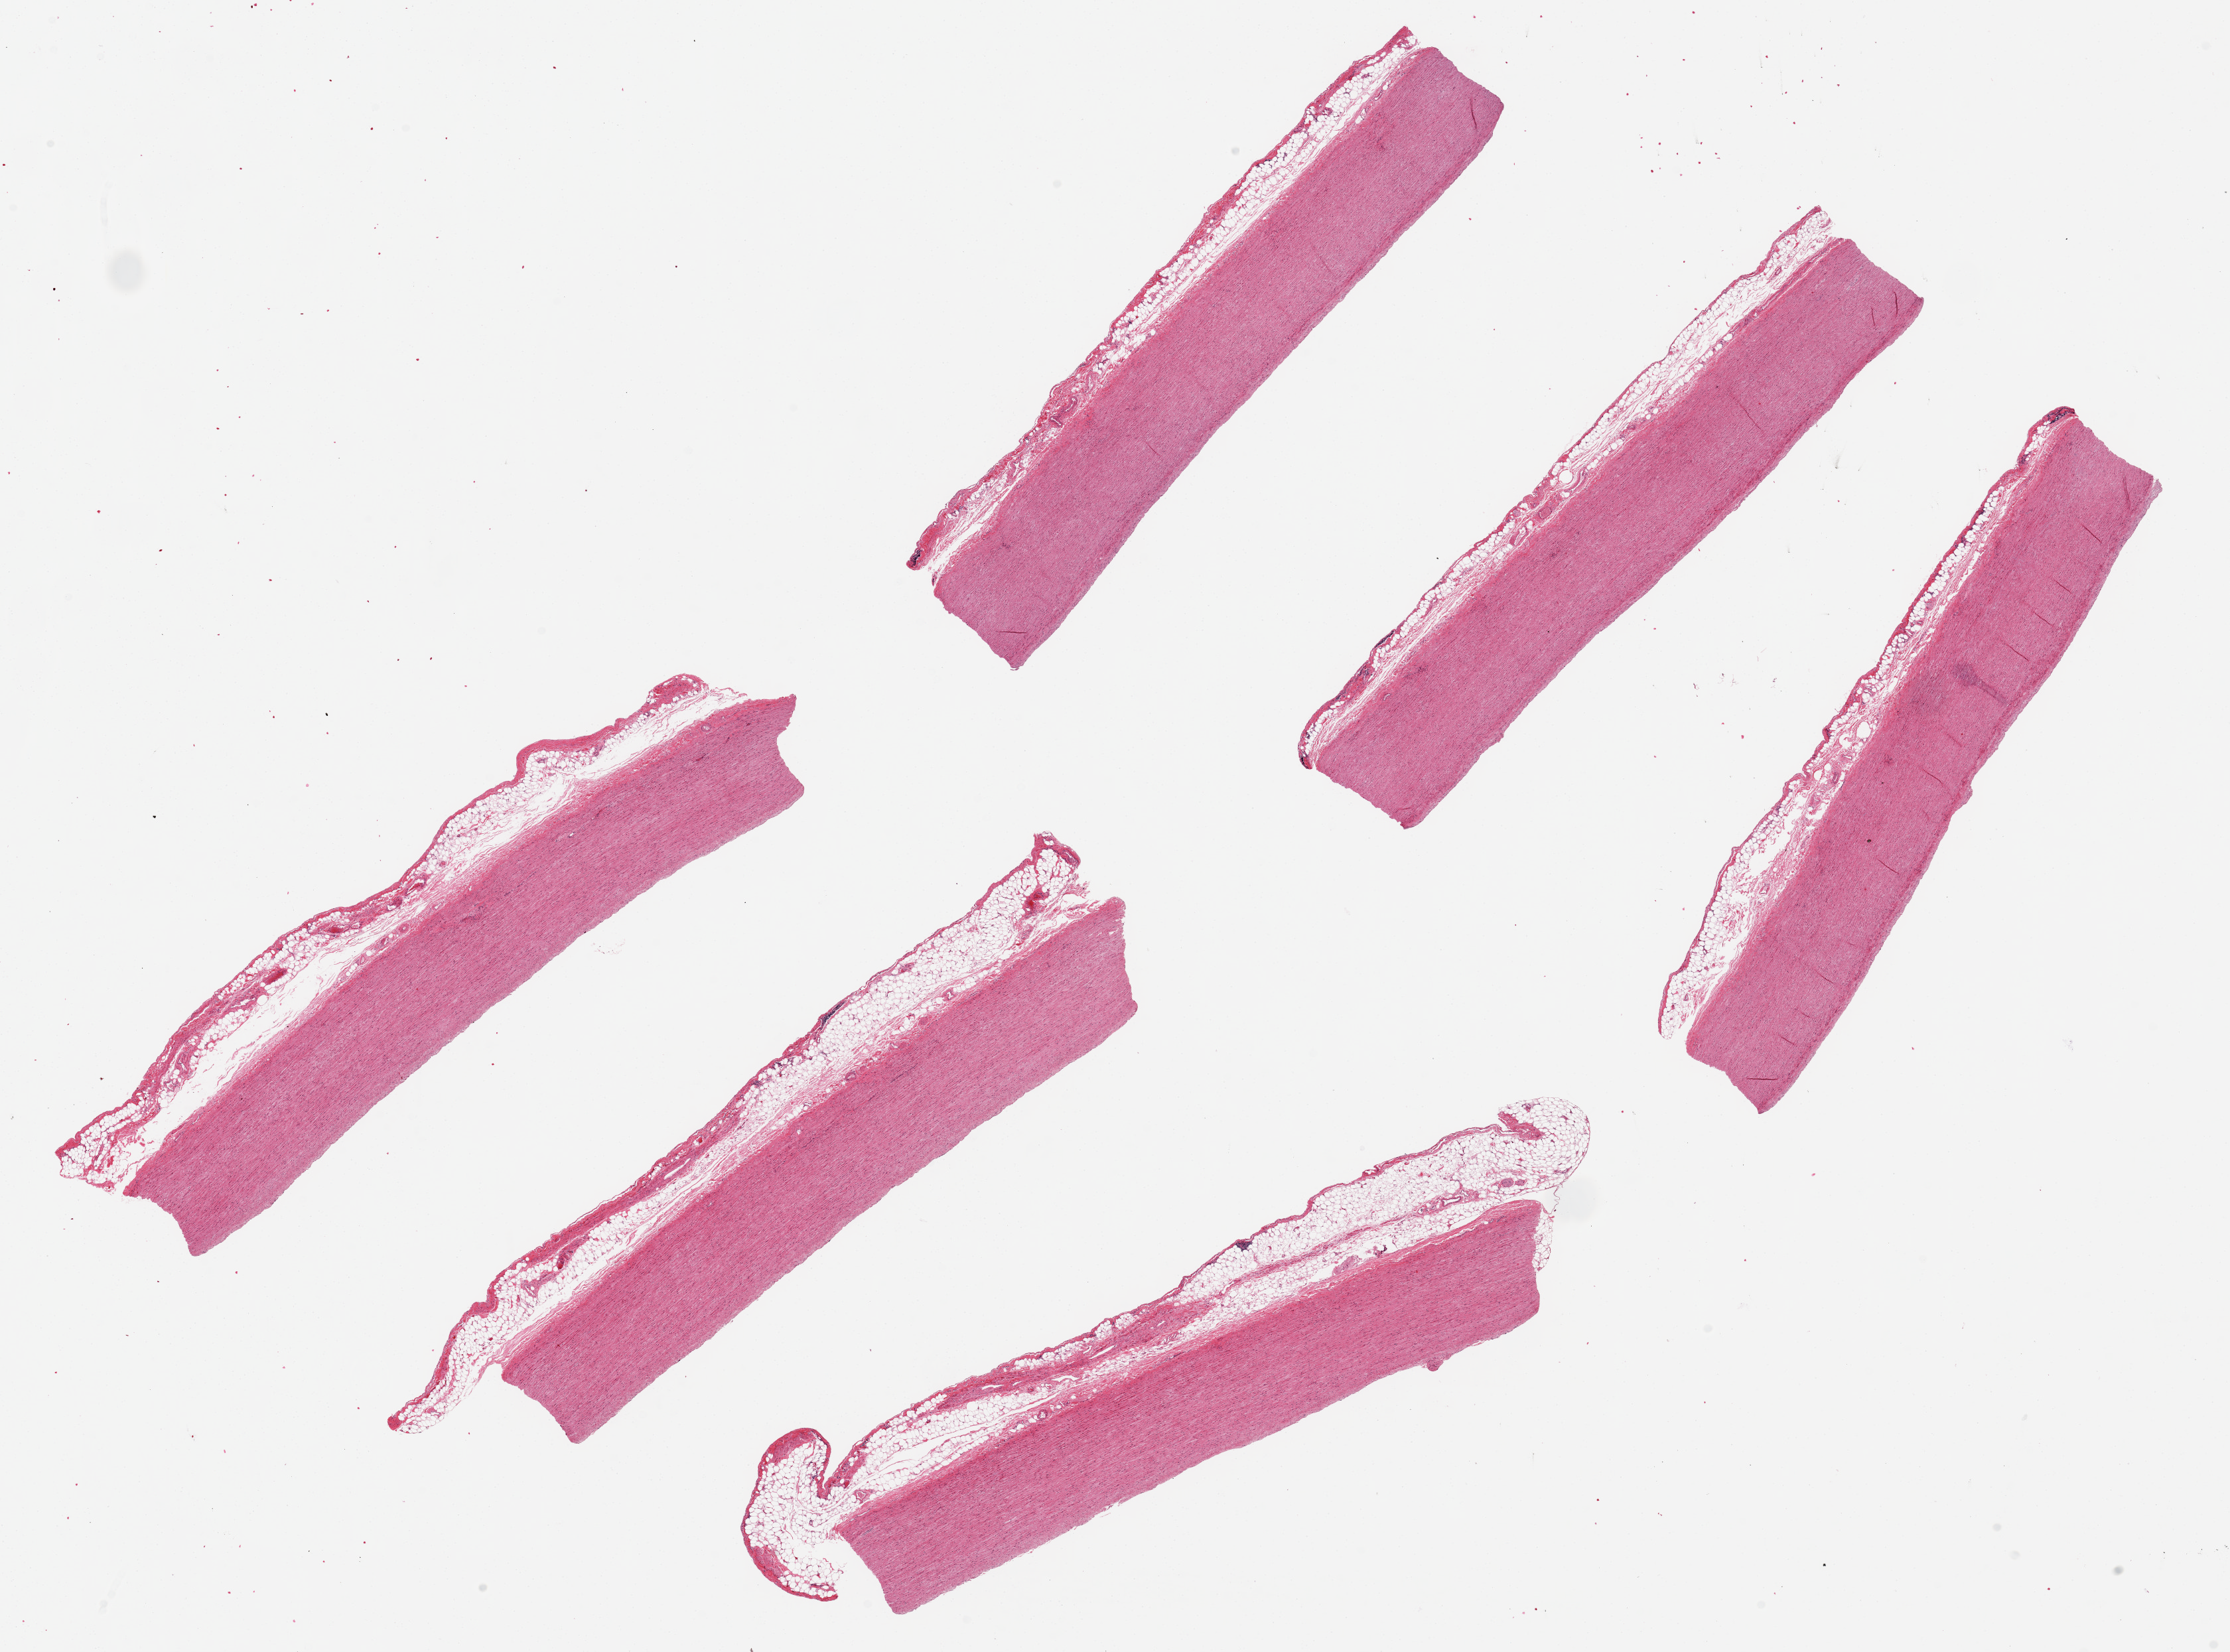
Digitized hematoxylin and eosin (H&E)-stained section, brightfield — shown as a low-resolution overview of the whole scanned area (about 26.6 x 19.7 mm, from a 20x scan); PAXgene-fixed paraffin-embedded (PFPE) section; target tissue: aorta; tissue donor sample. Donor sex: male.
Reviewer comment on this tissue sample: 6 ~9x1.5mm pieces, most with a 0.5mm layer of peri-aortic fat.